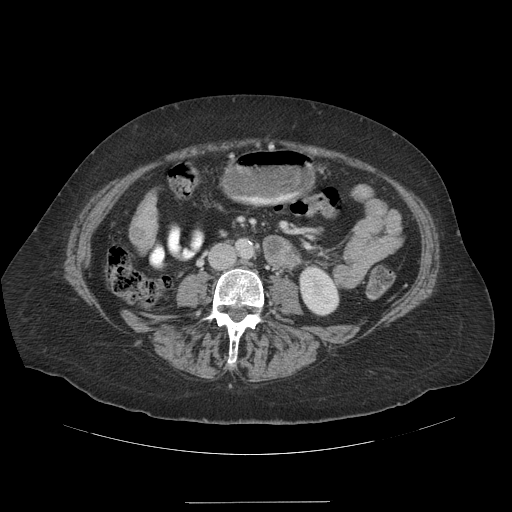
Contrast-enhanced abdominal CT (liver protocol), one axial slice; slice 28 of 99 in the series (ordered by position); reconstruction kernel STANDARD; 140 kVp; soft-tissue window (W 400 / L 40 HU); 512 × 512 image matrix, field of view 440 × 440 mm. Case-level facts recorded for this patient, not image findings: diagnosis: hepatocellular carcinoma (patient treated with transarterial chemoembolisation; whether this scan precedes or follows treatment is not stated here); TNM stage (as recorded): Stage-IVA; Child-Pugh class: A; tumour nodularity: multinodular.
Outlined on this slice (semi-automatic segmentation, software-assisted and operator-edited):
- liver parenchyma outside the tumour (the mass and vessels are separate outlines, so this box may not span the whole liver): bounding box (x1, y1, x2, y2) in pixels: (131, 196, 158, 240)